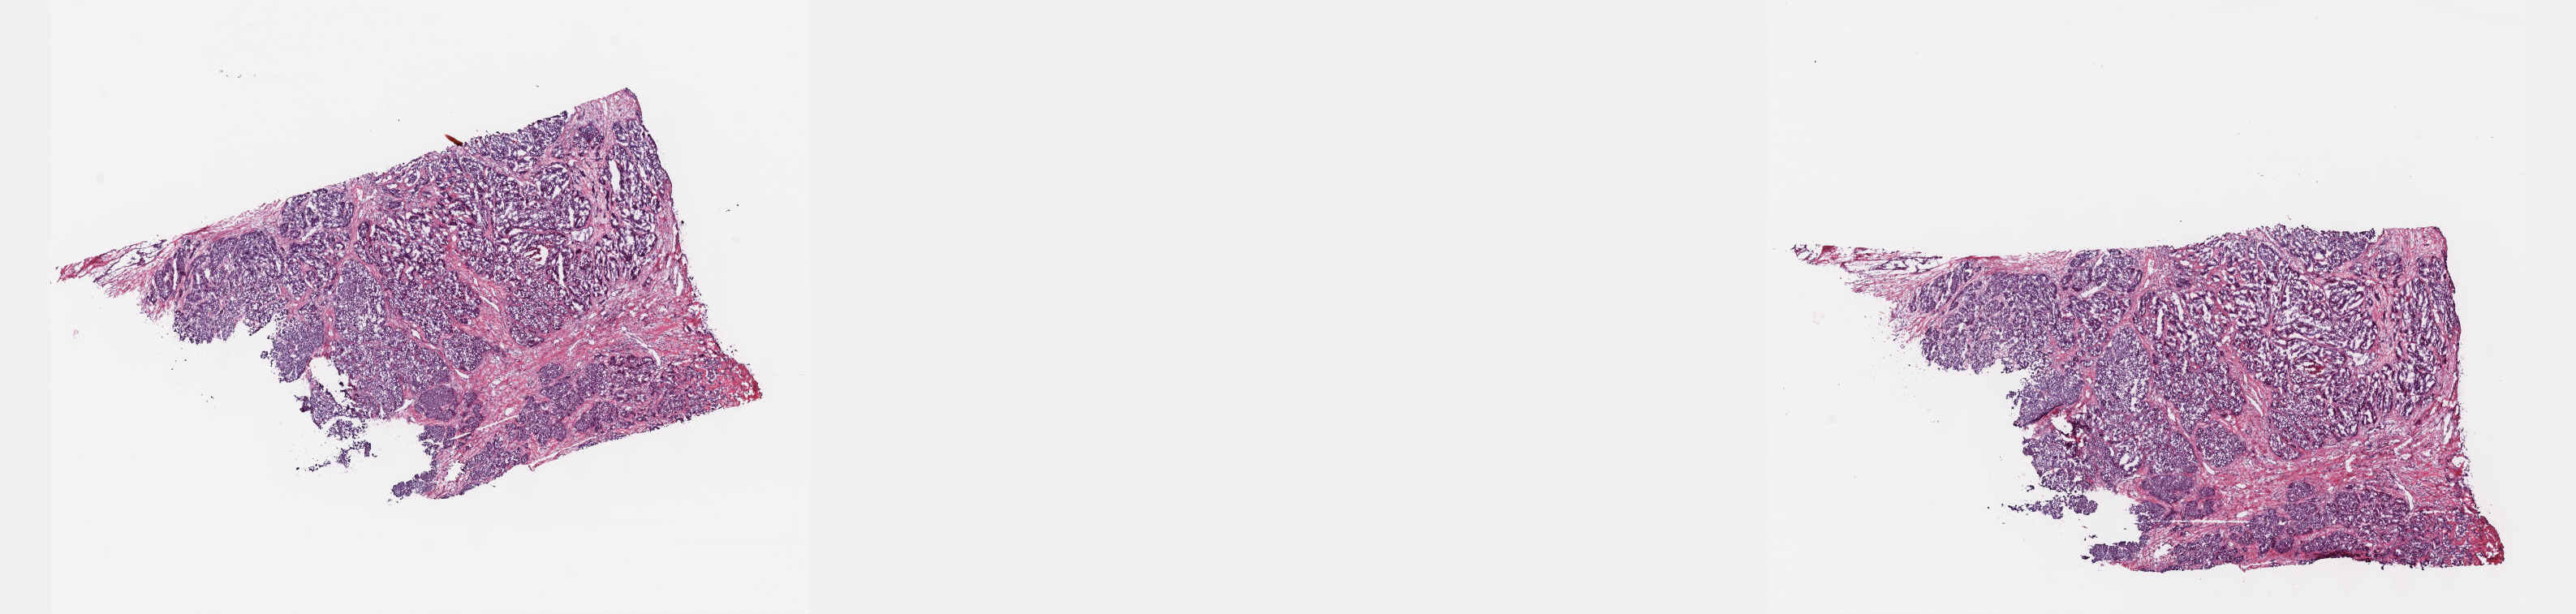
Whole-slide histology image, H&E — whole scanned area (about 25.7 x 6.1 mm, acquisition: 40x scan) shown as a low-resolution overview, frozen section from the top of the tissue portion, liver, primary tumour sample. Male patient; age at initial diagnosis 47 years. Histologic grade: G2 (moderately differentiated). Slide review estimates, as recorded: tumour cells 100%, tumour nuclei 70%, normal cells 0%, stromal cells 0%, necrosis 0%. Infiltration values recorded for this section: lymphocyte infiltration 3%, monocyte infiltration 0%, neutrophil infiltration 0%.
AJCC pathologic stage: II (6th edition). Pathologic diagnosis: Hepatocellular carcinoma, NOS.